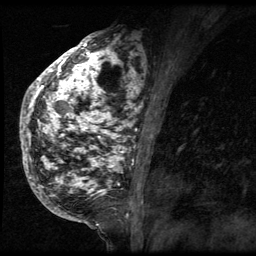
Breast MRI (dynamic contrast-enhanced), one sagittal slice; 3 images stored at this slice position (order not interpretable as contrast timing); 1.5 T; TE 4.2 ms, TR 9 ms; 256 × 256 image matrix, field of view 180 × 180 mm. Patient: female, 50 years. From the clinical record (not read from this slice): setting: breast cancer imaged before/during neoadjuvant chemotherapy; receptor status: triple-negative.
Annotated regions visible in this slice (semi-automatically segmented with operator editing):
- analysis volume of interest (the breast-tissue region the enhancement analysis was run in; not a lesion): bounding box [x1, y1, x2, y2] px = [24, 39, 140, 212]
- tumour enhancement mask (voxels above the 140 % enhancement threshold inside the analysis volume of interest): [24, 39, 140, 209]